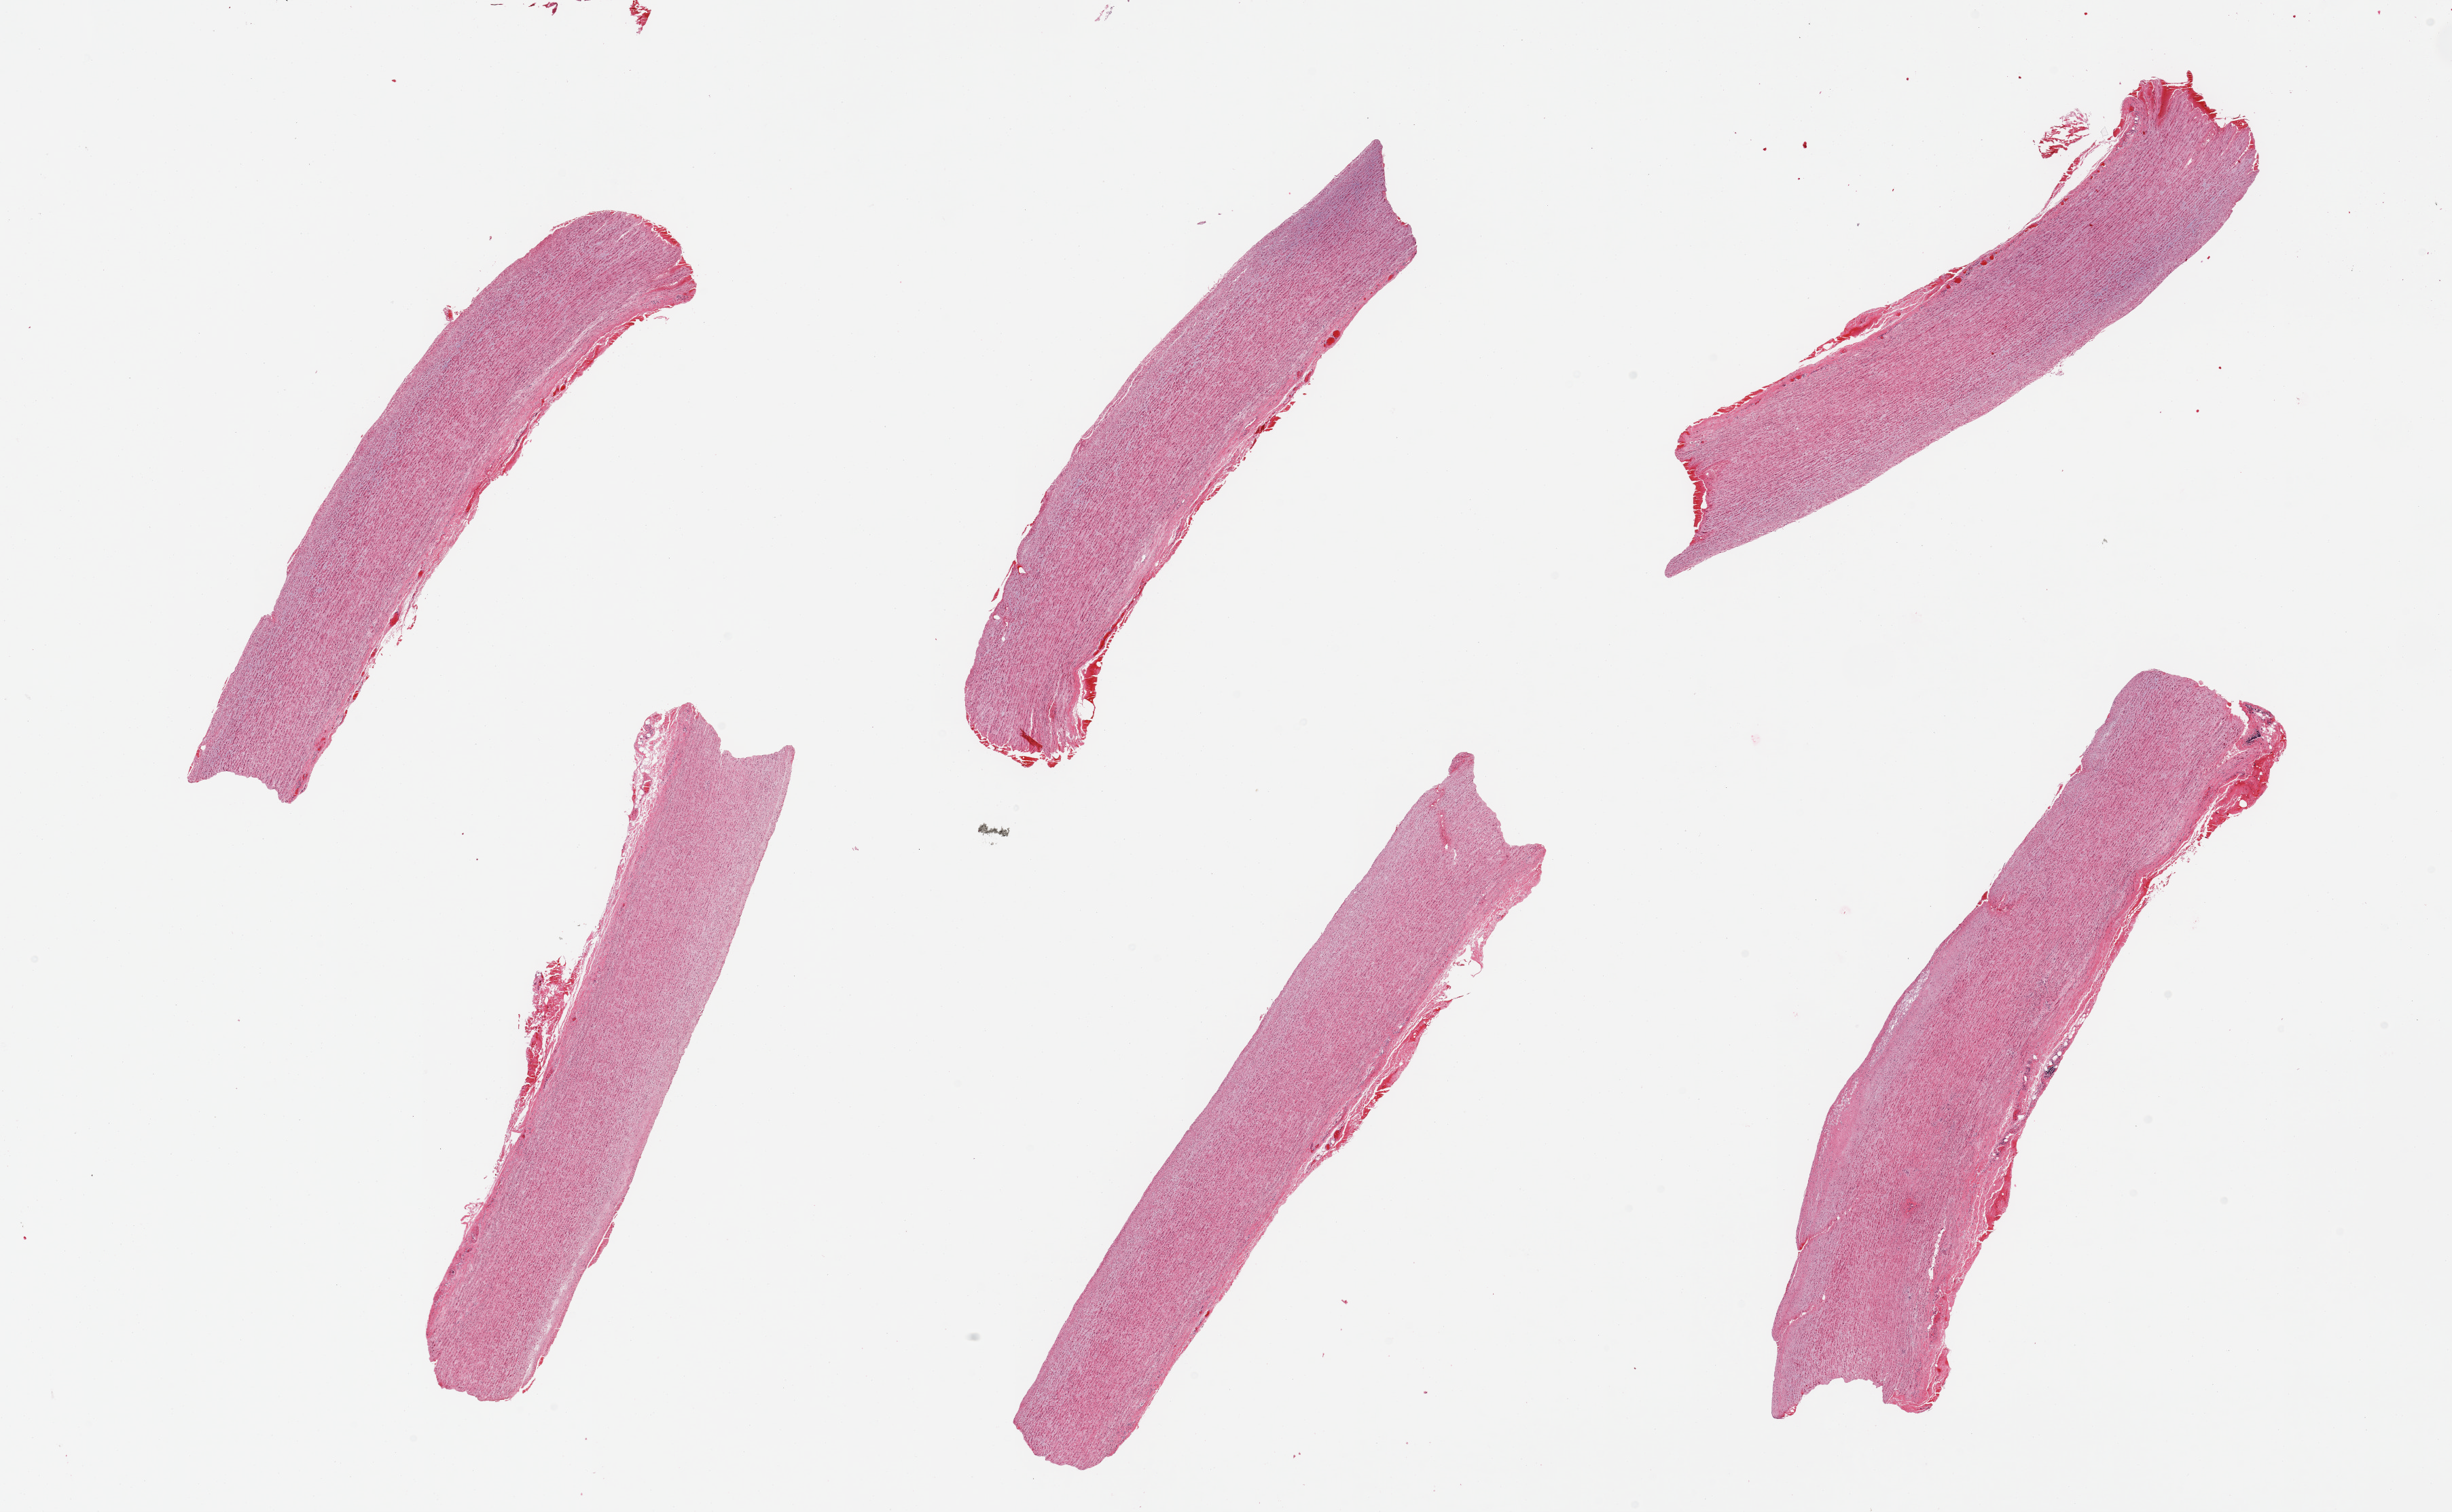
Whole-slide image, hematoxylin and eosin (H&E) stain — whole scanned area (about 28.5 x 17.6 mm) shown as a low-resolution overview. PAXgene-fixed paraffin-embedded (PFPE) section. Target tissue: aorta. Donor tissue sample. Donor: female.
Review note (as recorded): 6 pieces, minimal atherosis.